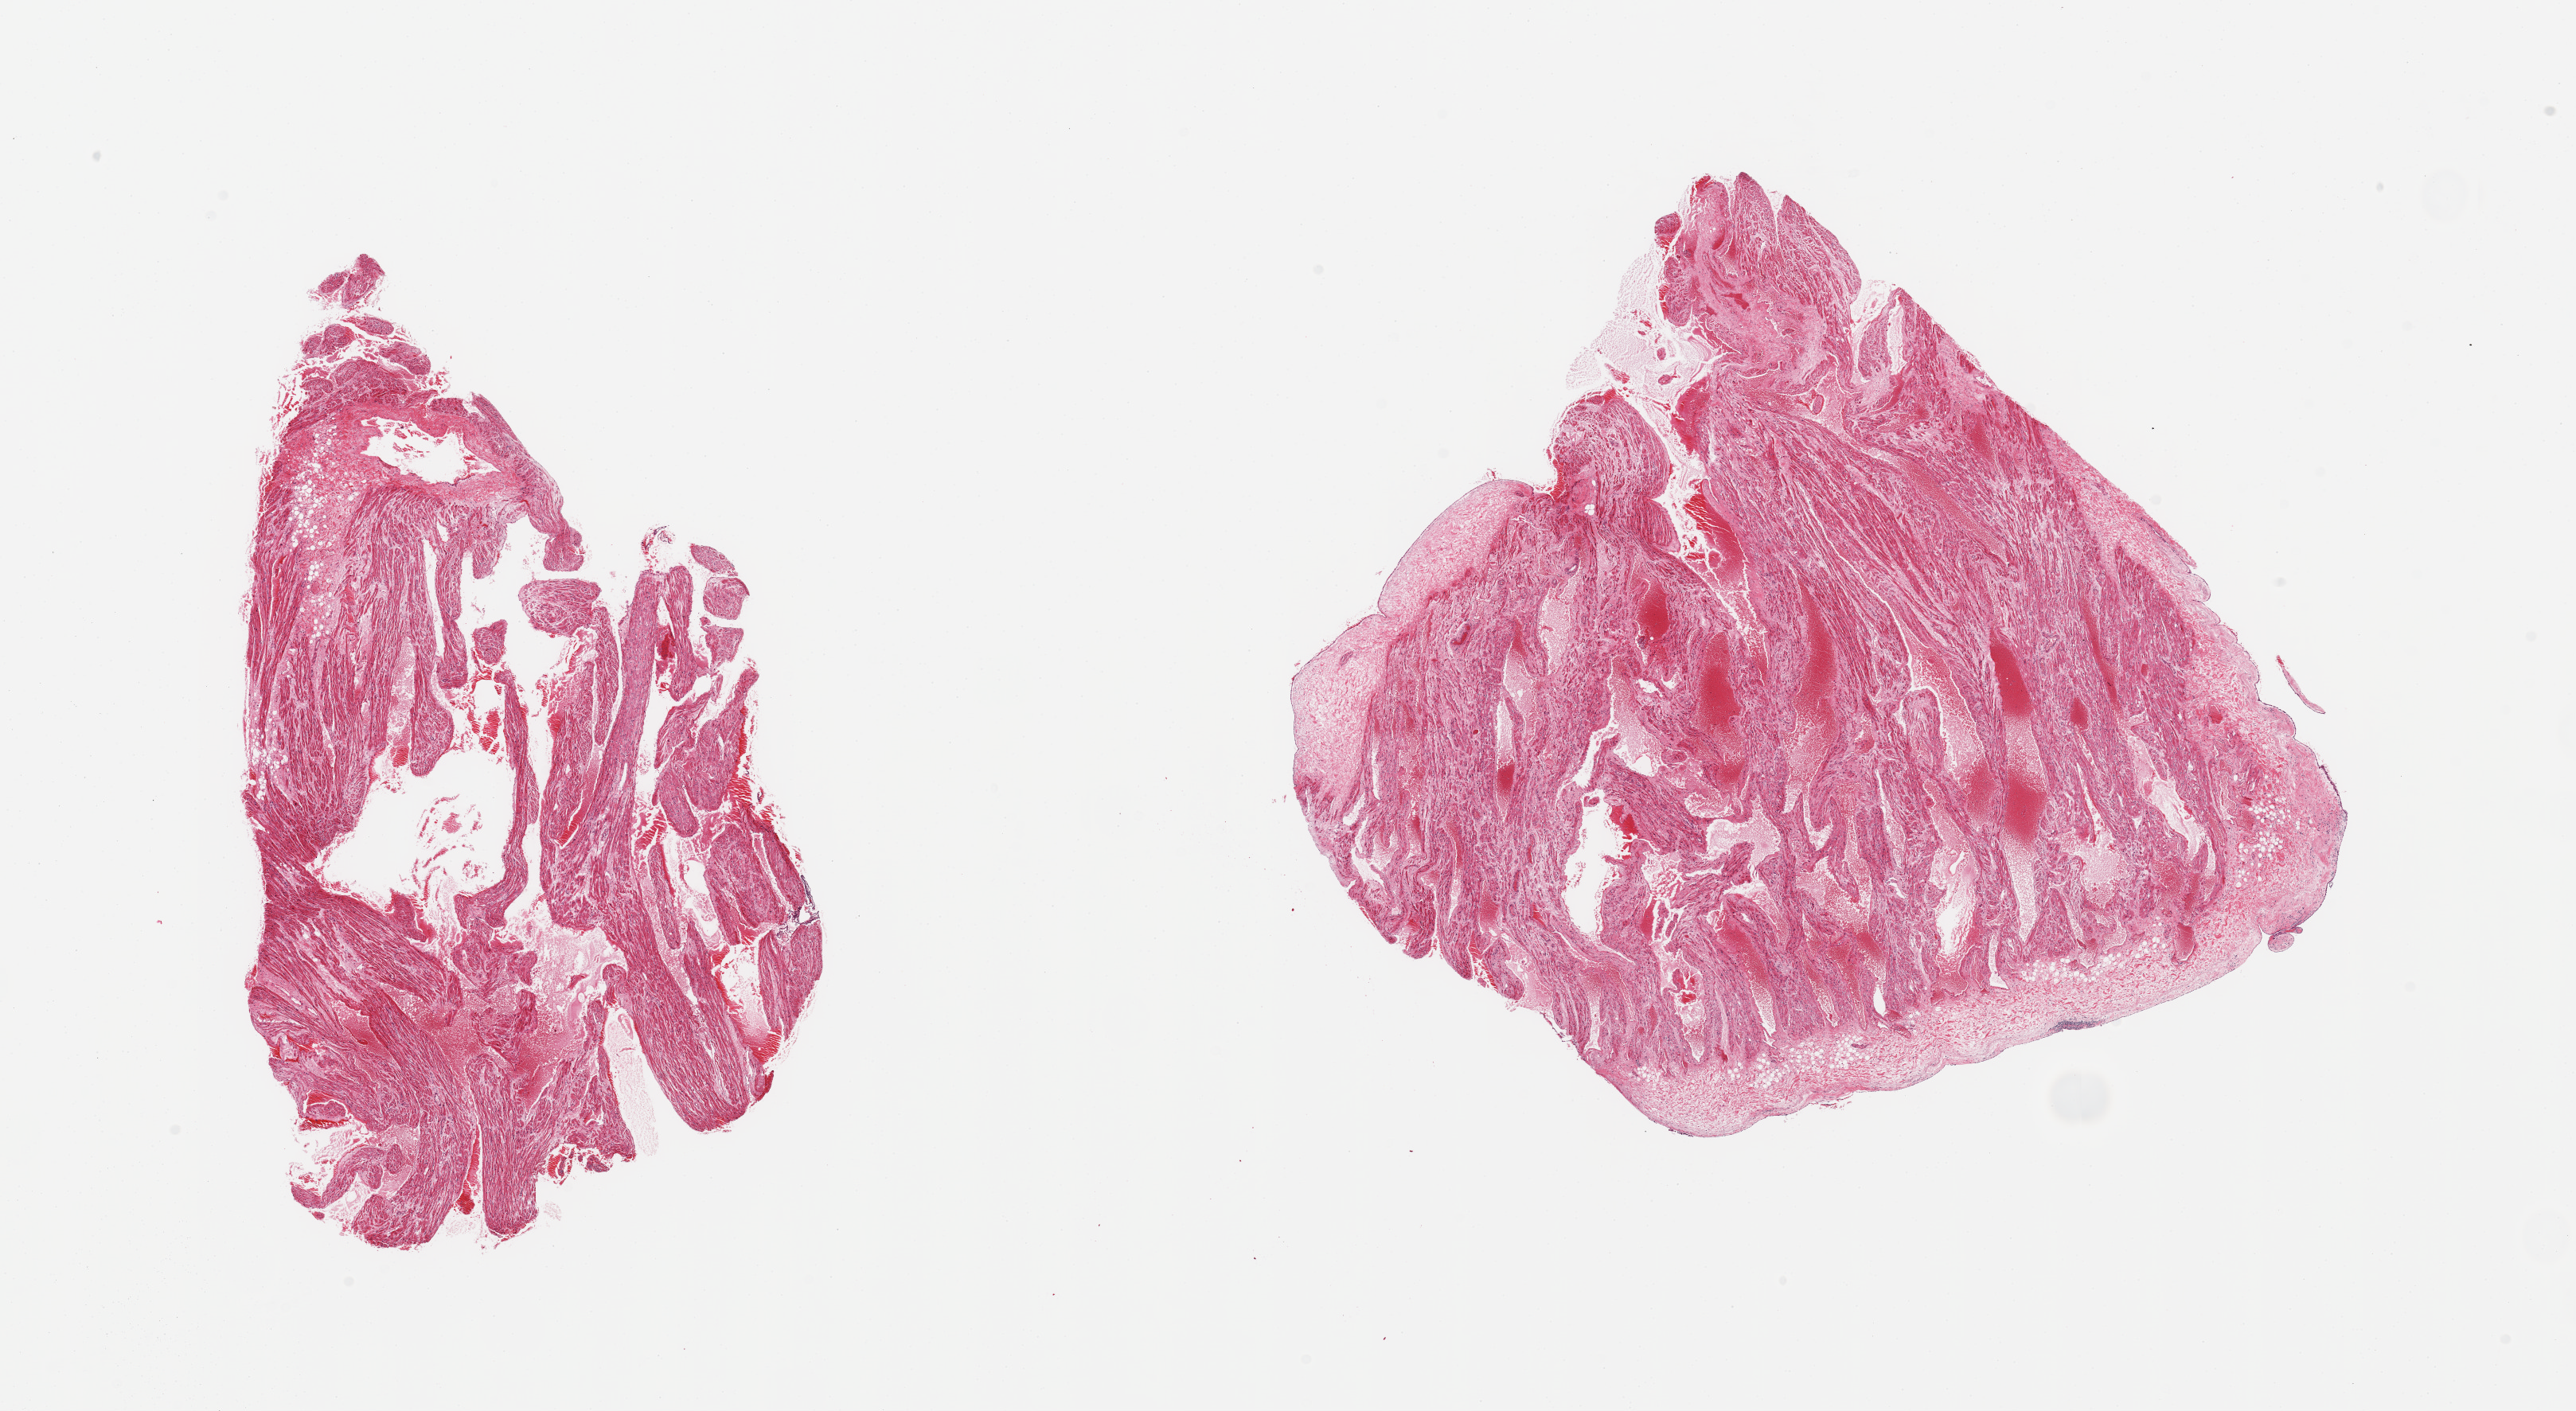
Digitized H&E-stained section — whole scanned area (about 25.6 x 14.0 mm, from a 20x scan) shown as a low-resolution overview, PAXgene-fixed paraffin-embedded (PFPE) section, sampled site (target tissue): auricular appendage, donor tissue sample. Male donor.
Reviewer comment on this tissue sample: 2 pieces, no abnormalities.